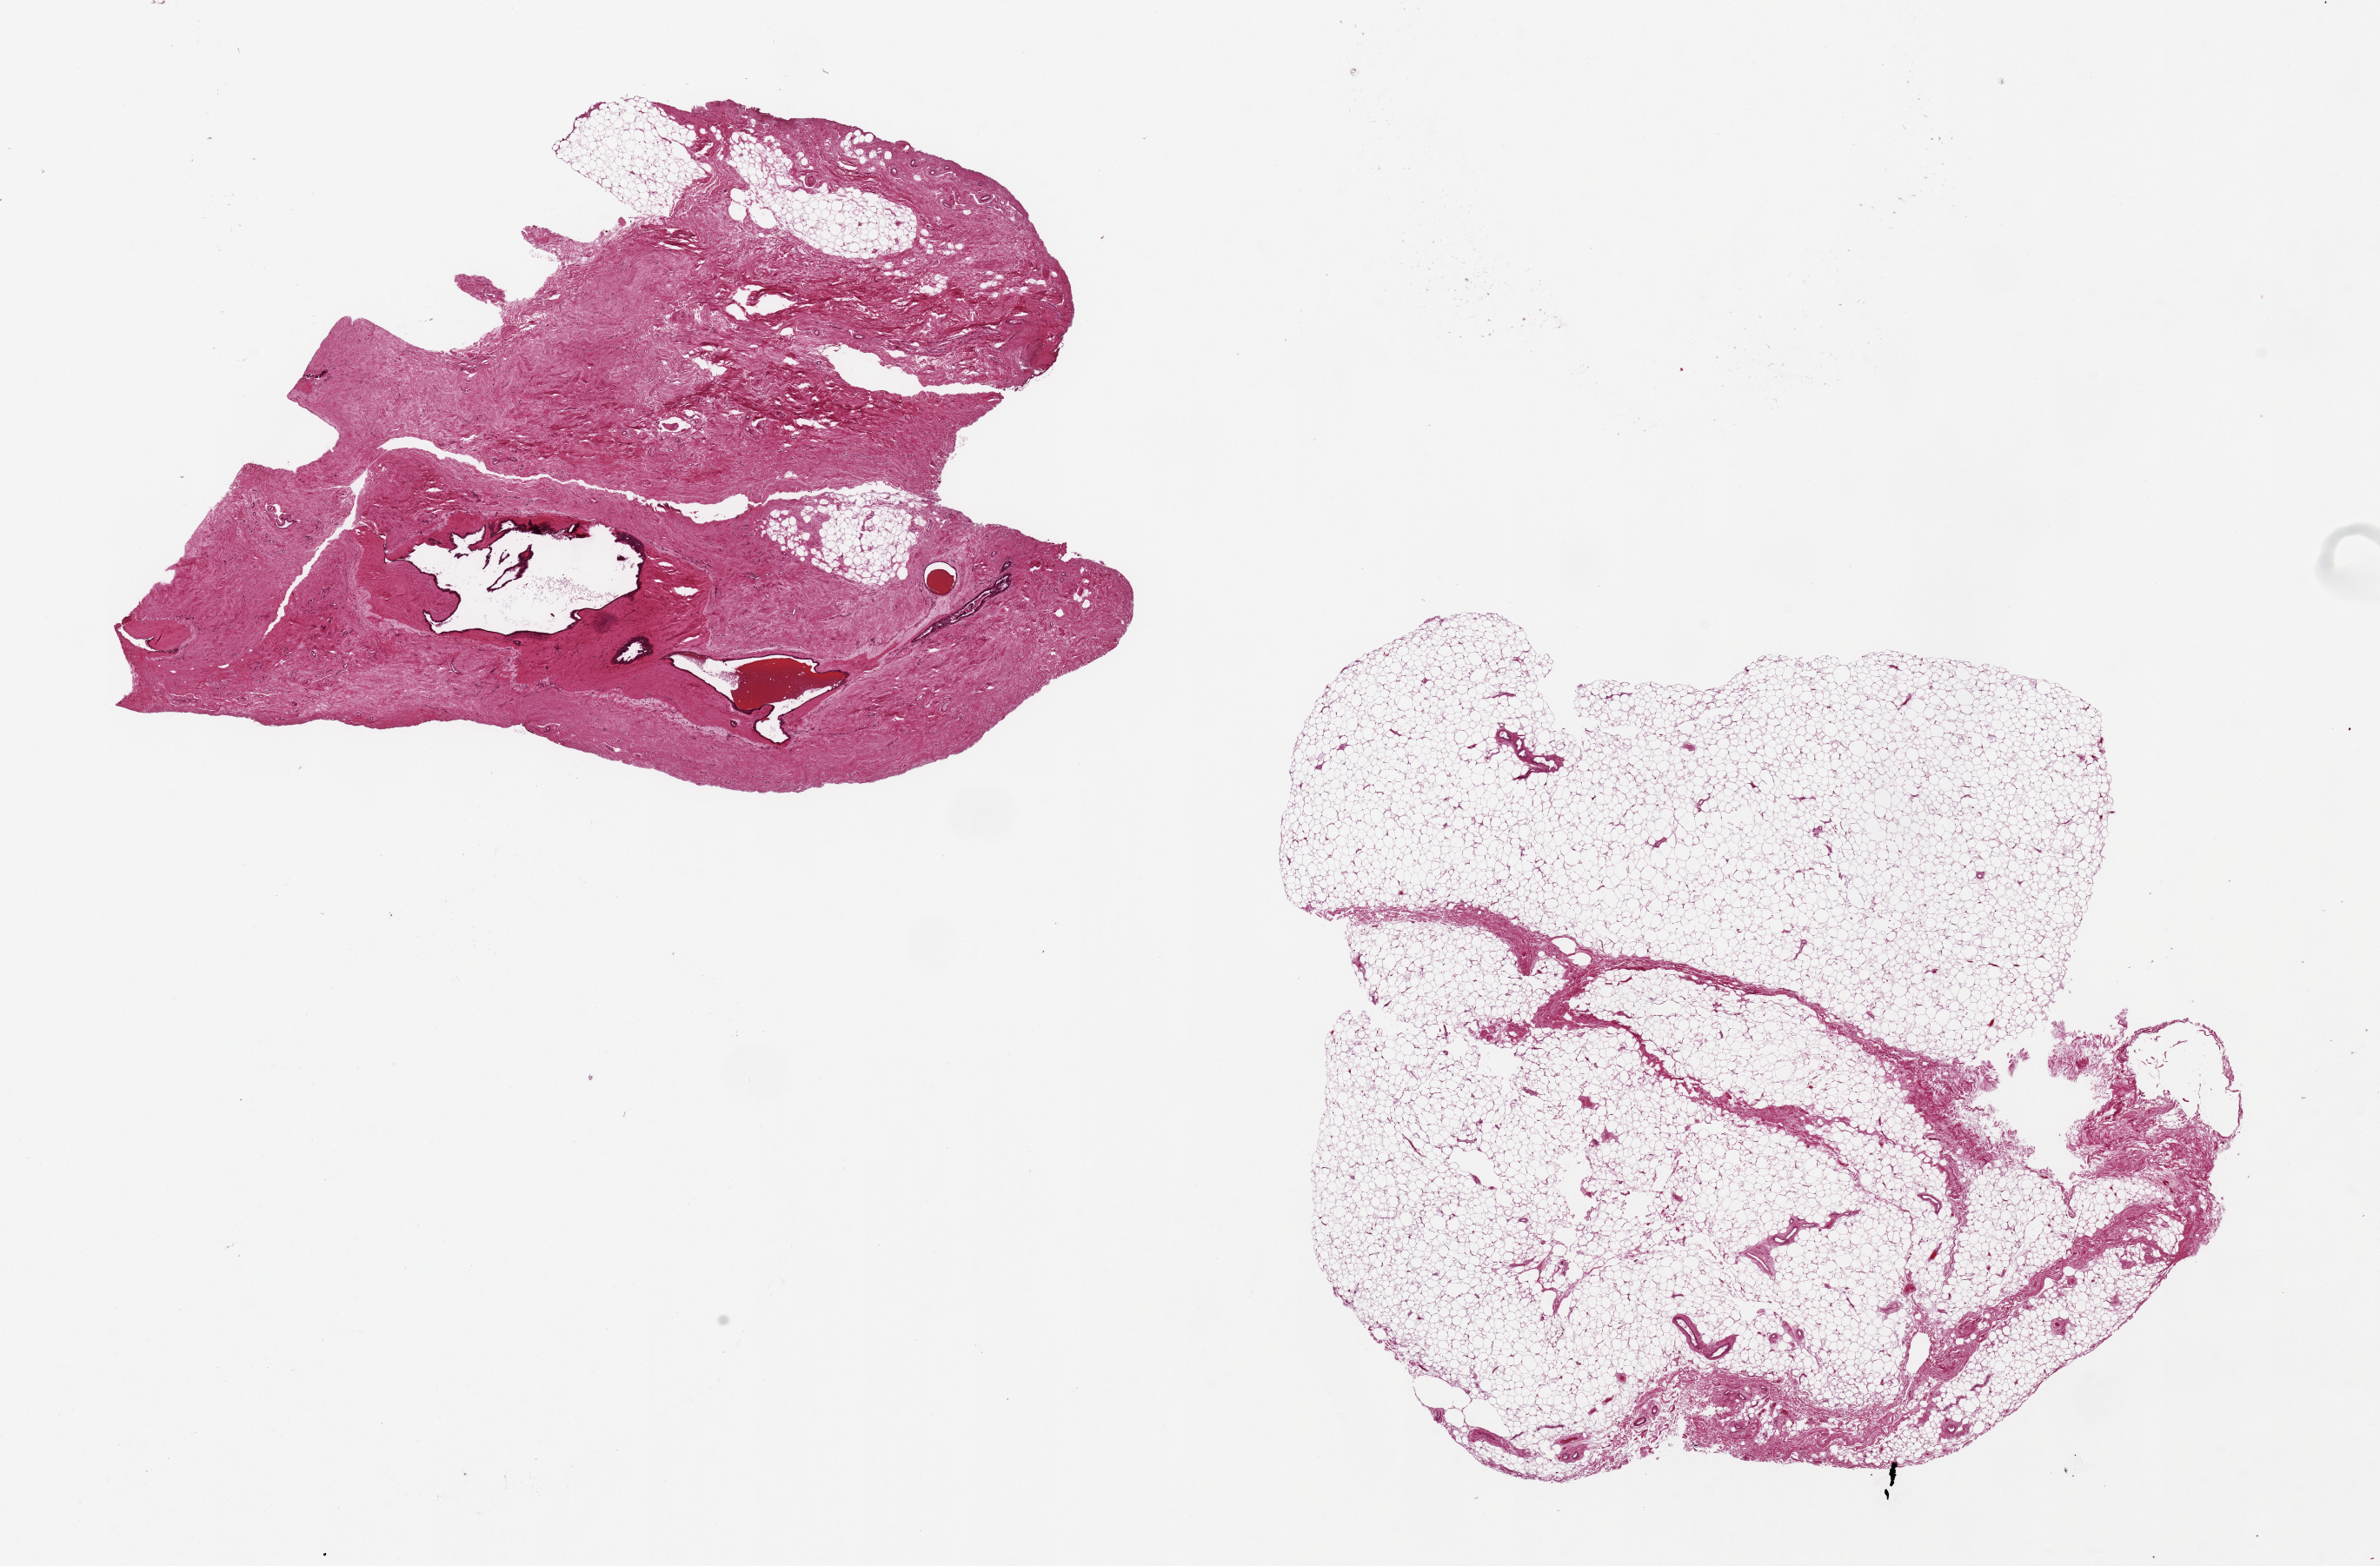
H&E whole-slide image, whole scanned area (about 21.7 x 14.3 mm, acquisition: 20x scan) shown as a low-resolution overview, PAXgene-fixed, paraffin-embedded tissue, target tissue: breast, tissue donor sample. Donor: female.
Pathologist's review note for this sample: 2 pieces: 8x7 mm with large ducts and fibrous stroma, no lobules; 8x8 mm: all adipose, no lobules.